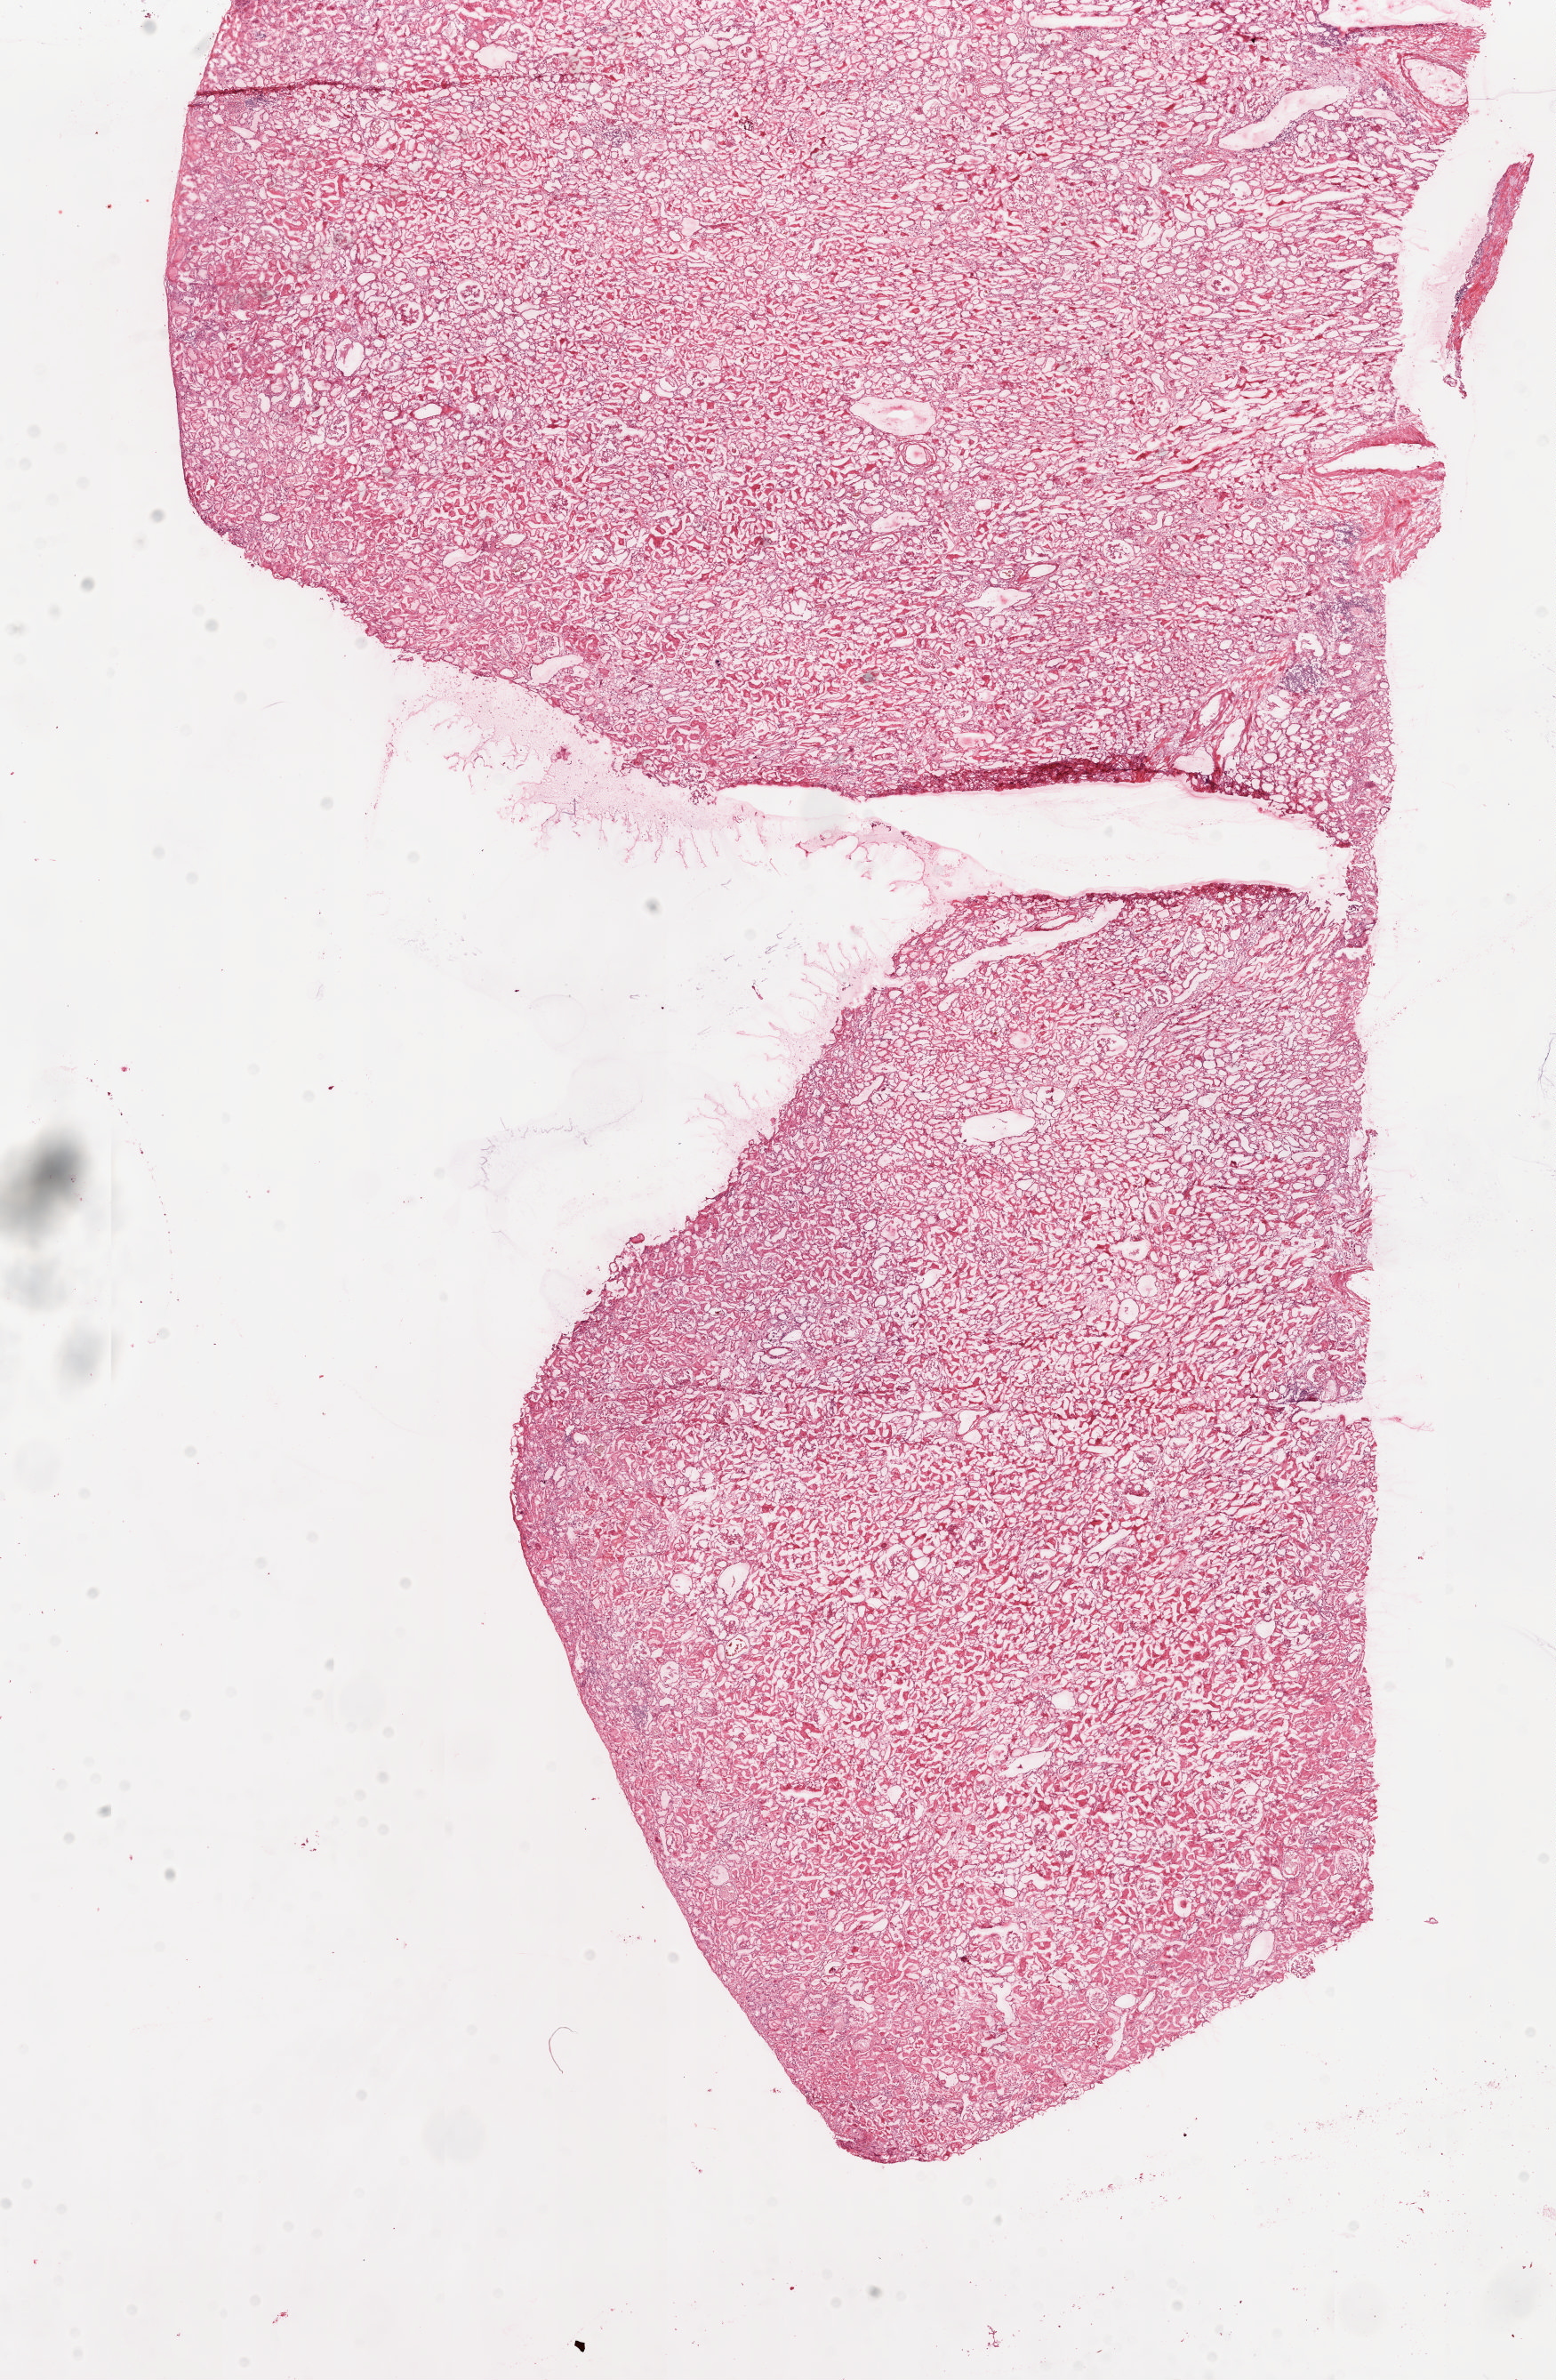
Whole-slide histology image, H&E — low-resolution overview of the scanned area, about 13.9 x 21.2 mm; frozen section from the top of the tissue portion; sample: solid tissue normal (non-tumour tissue), kidney. Male patient; age at initial diagnosis 58 years.
This section: solid tissue normal sample (biorepository sample class). Patient diagnosis: Clear cell adenocarcinoma, NOS.